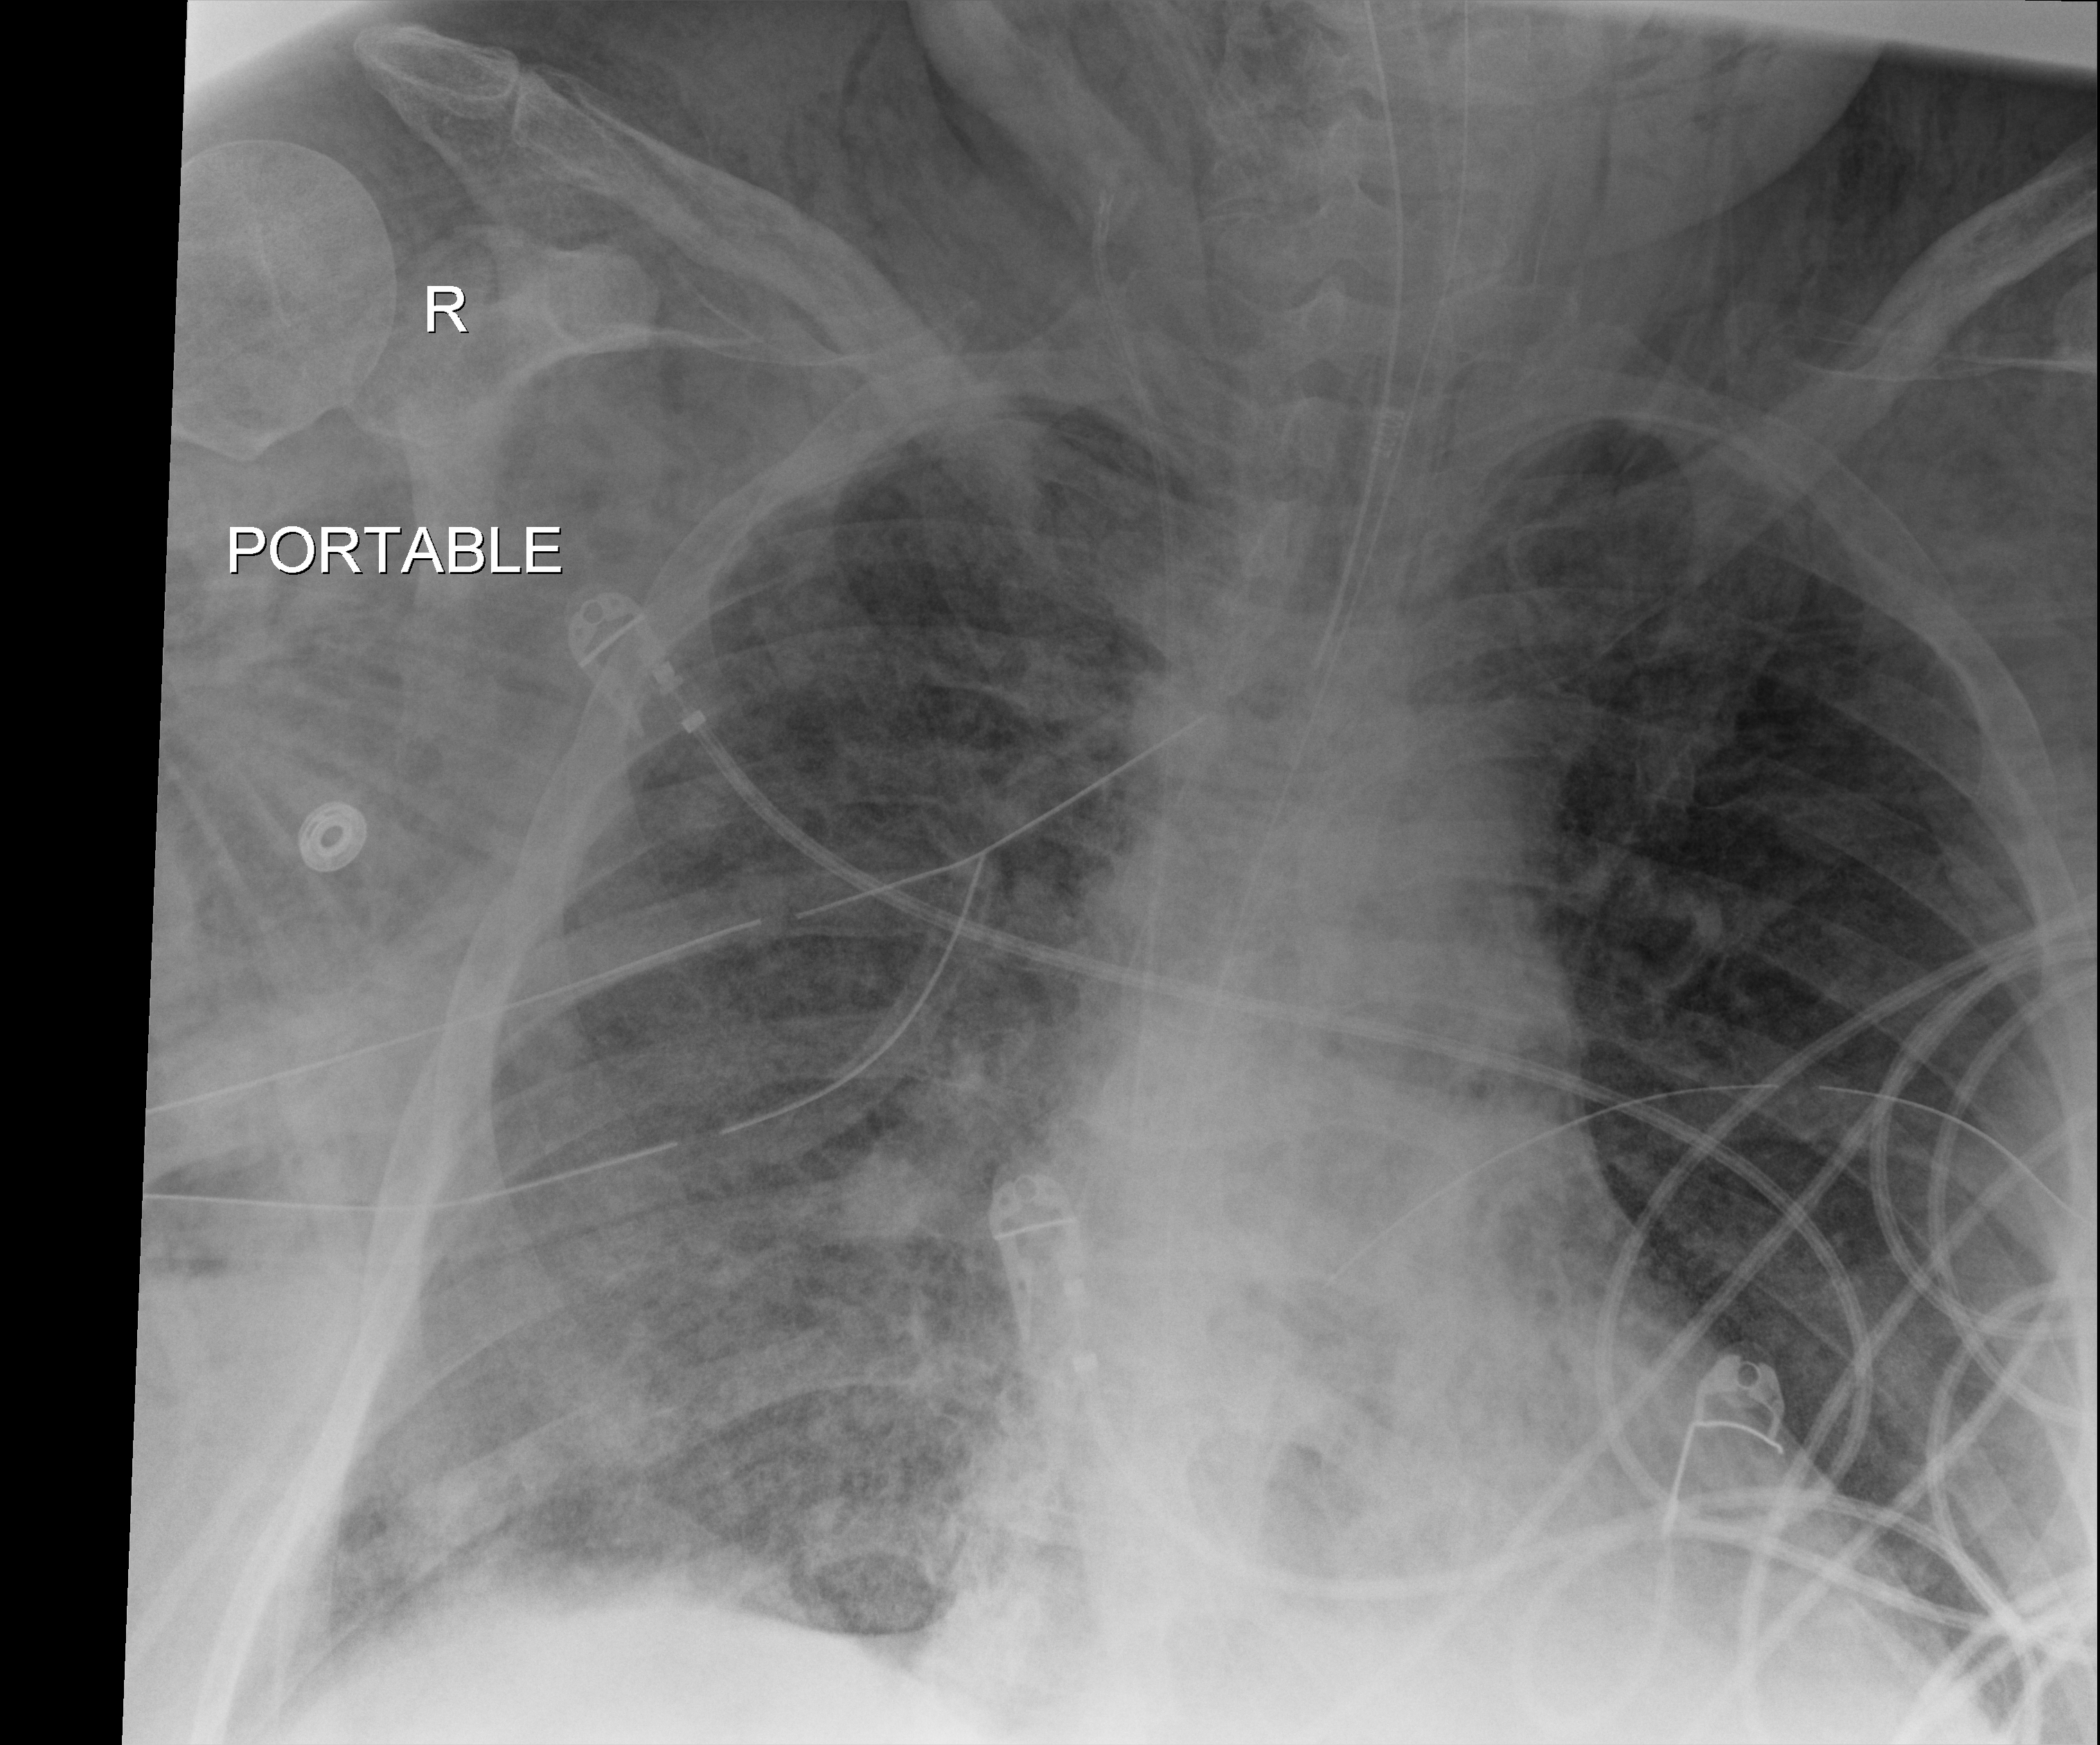
Chest X-ray (portable); anteroposterior (AP) projection. Patient hospitalised with COVID-19, aged 18–59 years.
Hospital-stay facts (about this admission, not read from this image; timing relative to this image not recorded):
- admitted to intensive care during this hospital stay: yes
- mechanically ventilated during this hospital stay: yes